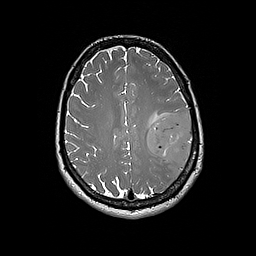
Brain MRI from a brain-tumour surgery series, one axial slice. Position 72 of 192 along the scan axis. 256 × 256 image matrix, field of view 250 × 250 mm. Case-level facts recorded for this patient, not image findings: histopathology: Glioblastoma; WHO grade: 4; IDH mutation: no.
Annotated regions visible in this slice (manually delineated by an expert):
- tumour: bounding box <147,114,193,165> (left, top, right, bottom; pixels)